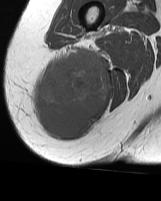
MRI of an extremity soft-tissue mass, one axial slice; position 21 of 70 along the scan axis; MR volume resampled by the dataset authors to the PET/CT grid (not the native acquisition matrix); 161 × 201 image matrix, field of view 157 × 196 mm. Female patient. Case-level facts recorded for this patient, not image findings: histological type: synovial sarcoma; grade: intermediate; site of the primary tumour: right buttock.
Annotated regions visible in this slice (expert contour drawn on MRI and transferred to this co-registered scan by the dataset authors):
- gross tumour volume including surrounding oedema: box from (x=33, y=45) to (x=109, y=139) px
- gross tumour volume (mass): (x=33, y=52)–(x=109, y=139)